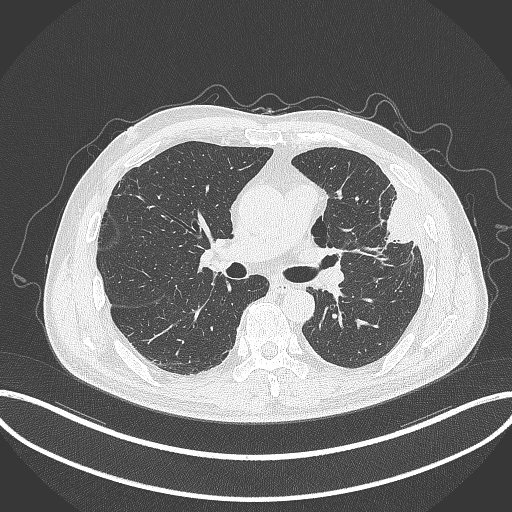
Chest CT, one axial slice. Slice 191 of 382 in the series (ordered by position). Reconstruction kernel B70f. 120 kVp. Lung window (W 1500 / L -600 HU). 1 mm slice thickness. 512 × 512 image matrix, field of view 415 × 415 mm. Male patient, age 64 years. From the clinical record (not read from this slice): clinical TNM (as recorded): T4 N1 M0.
Annotated regions visible in this slice (rectangle marked by the reading radiologist):
- lung tumour (recorded histology: adenocarcinoma): box from (x=369, y=197) to (x=417, y=255) px